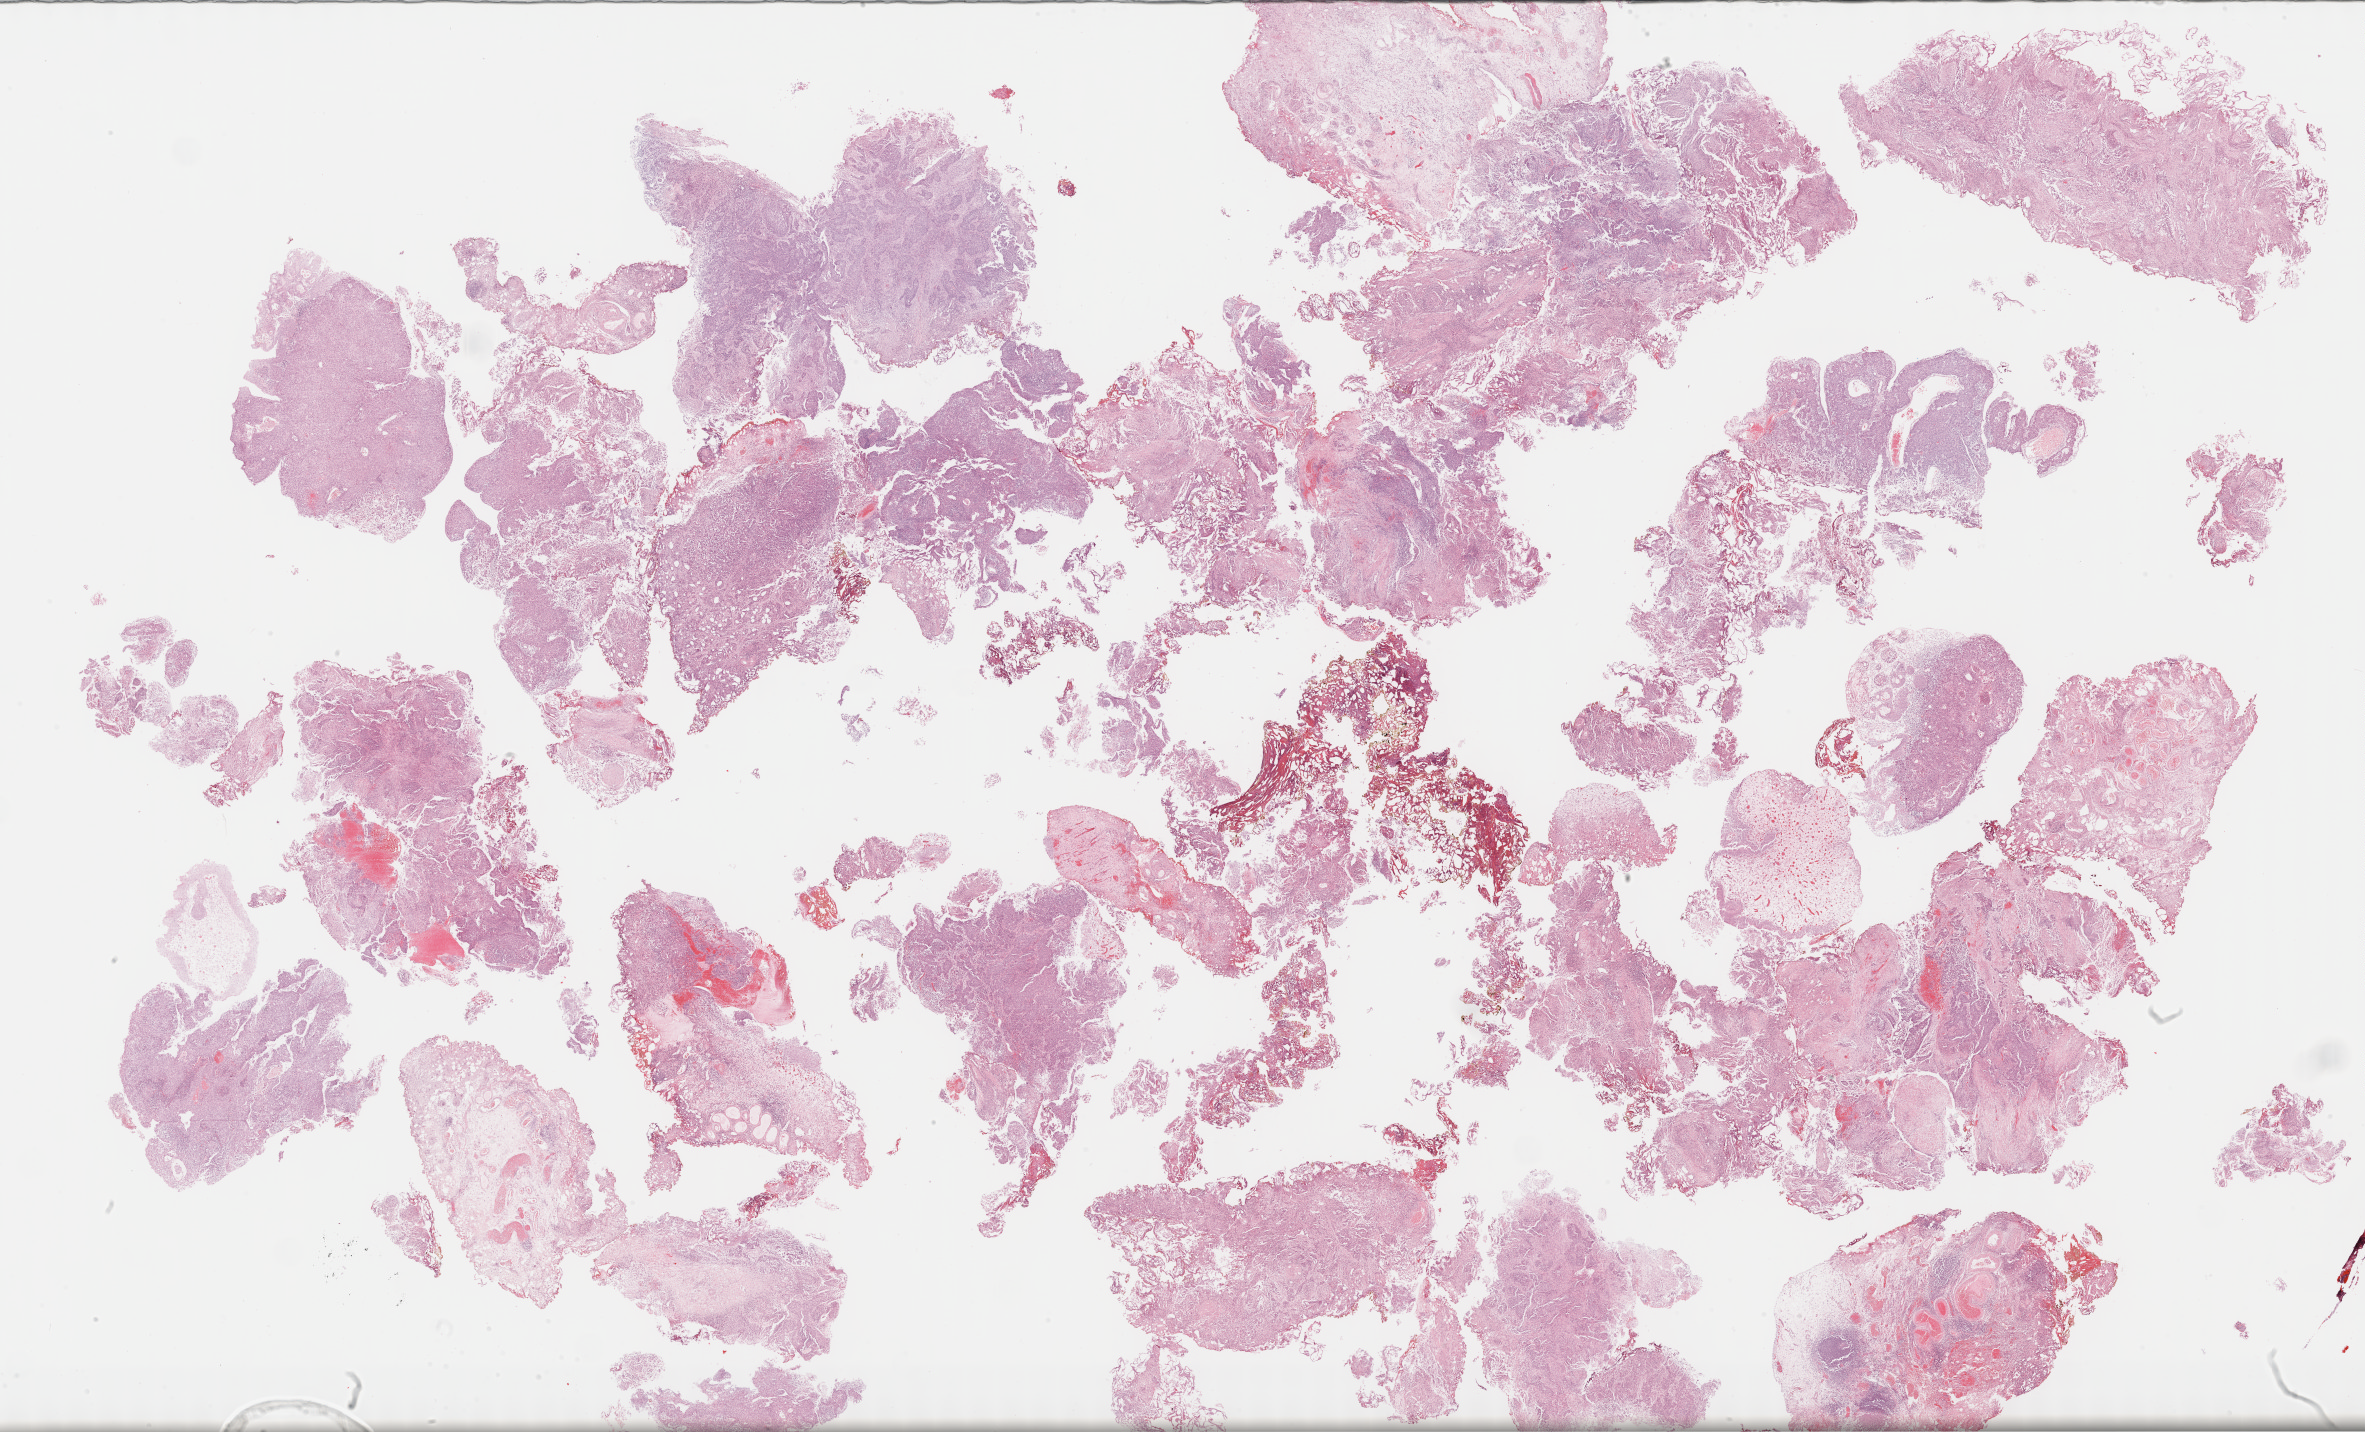
Digitized Hematoxylin and eosin (H&E) stained tissue section (whole slide) — a low-resolution overview of the entire scanned area, about 38.3 x 23.2 mm (acquisition: 40x scan). Formalin-fixed paraffin-embedded (FFPE) diagnostic section. Primary tumour sample from the bladder. Female patient; age at initial diagnosis 76 years. Histologic grade: high grade.
AJCC pathologic stage: II (7th edition). Pathologic diagnosis: Transitional cell carcinoma.